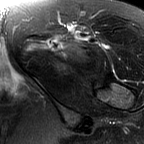
MRI of an extremity soft-tissue mass, one axial slice; slice 51 of 60 in the series (ordered by position); T2-weighted fat-saturated; MR volume resampled by the dataset authors to the PET/CT grid (not the native acquisition matrix); 3.27 mm slice thickness; 144 × 144 image matrix, field of view 141 × 141 mm. Female patient. Case-level facts recorded for this patient, not image findings: histological type: pleiomorphic leiomyosarcoma; grade: intermediate; site of the primary tumour: left thigh.
Outlined on this slice (expert contour drawn on MRI and transferred to this co-registered scan by the dataset authors):
- gross tumour volume including surrounding oedema: bounding box <25,42,48,55> (left, top, right, bottom; pixels)